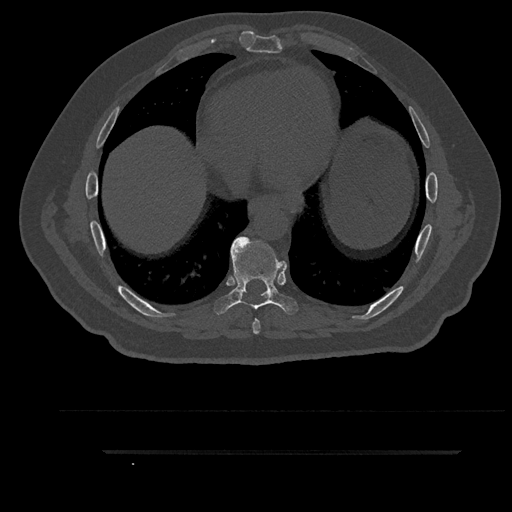
CT including the spine, one axial slice; 120 kVp; bone window (W 1800 / L 400 HU); 512 × 512 image matrix, field of view 432 × 432 mm. Male patient, age 63 years. Case-level facts recorded for this patient, not image findings: primary cancer: renal; vertebrae with lytic lesions (as recorded): T8.
Annotated regions visible in this slice (semi-automatically segmented with operator editing):
- T7 vertebra: bounding box (x1, y1, x2, y2) in pixels: (252, 318, 261, 334)
- T8 vertebra: (214, 236, 298, 315)